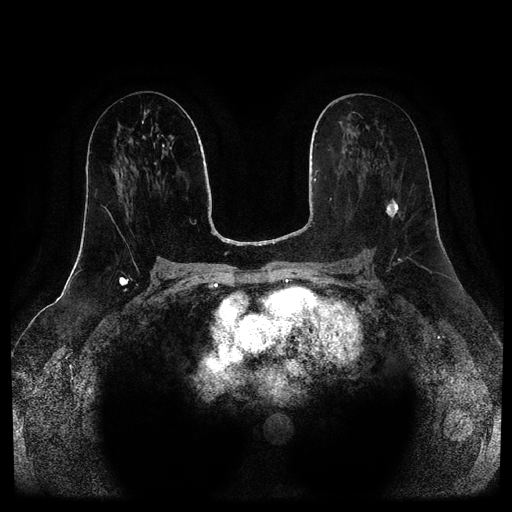
Breast MRI (dynamic contrast-enhanced, multi-phase), one axial slice; position 43 of 116 along the scan axis; dynamic contrast-enhanced series, time point 2 of 5 at this slice position (early post-contrast); 1.5 T; TE 2.6 ms, TR 5.2 ms; 2 mm slice thickness; 512 × 512 image matrix, field of view 380 × 380 mm. Female patient, age 57 years.
Annotated regions visible in this slice (semi-automatically segmented with operator editing):
- breast lesion (labelled 'tumour' in the annotation; benign lesions carry a separate 'benign' label): bounding box <386,199,399,218> (left, top, right, bottom; pixels)